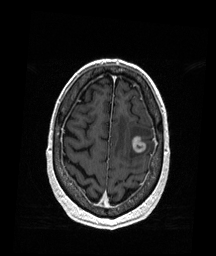
Brain MRI from a brain-tumour surgery series, one axial slice; slice 45 of 176 in the series (ordered by position); T1-weighted post-contrast; 1 mm slice thickness; 216 × 256 image matrix, field of view 211 × 250 mm. From the clinical record (not read from this slice): histopathology: Metastatic Melanoma.
Outlined on this slice (outlined manually by an expert reader):
- tumour: bounding box [x1, y1, x2, y2] px = [131, 136, 146, 153]